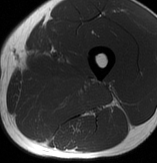
MRI of an extremity soft-tissue mass, one axial slice. MR volume resampled by the dataset authors to the PET/CT grid (not the native acquisition matrix). 3.27 mm slice thickness. 157 × 163 image matrix, field of view 153 × 159 mm. Male patient. Case-level facts recorded for this patient, not image findings: histological type: extraskeletal osteosarcoma; grade: high; site of the primary tumour: left adductur.
Outlined on this slice (expert contour drawn on MRI and transferred to this co-registered scan by the dataset authors):
- gross tumour volume (mass): bounding box <15,67,114,130> (left, top, right, bottom; pixels)